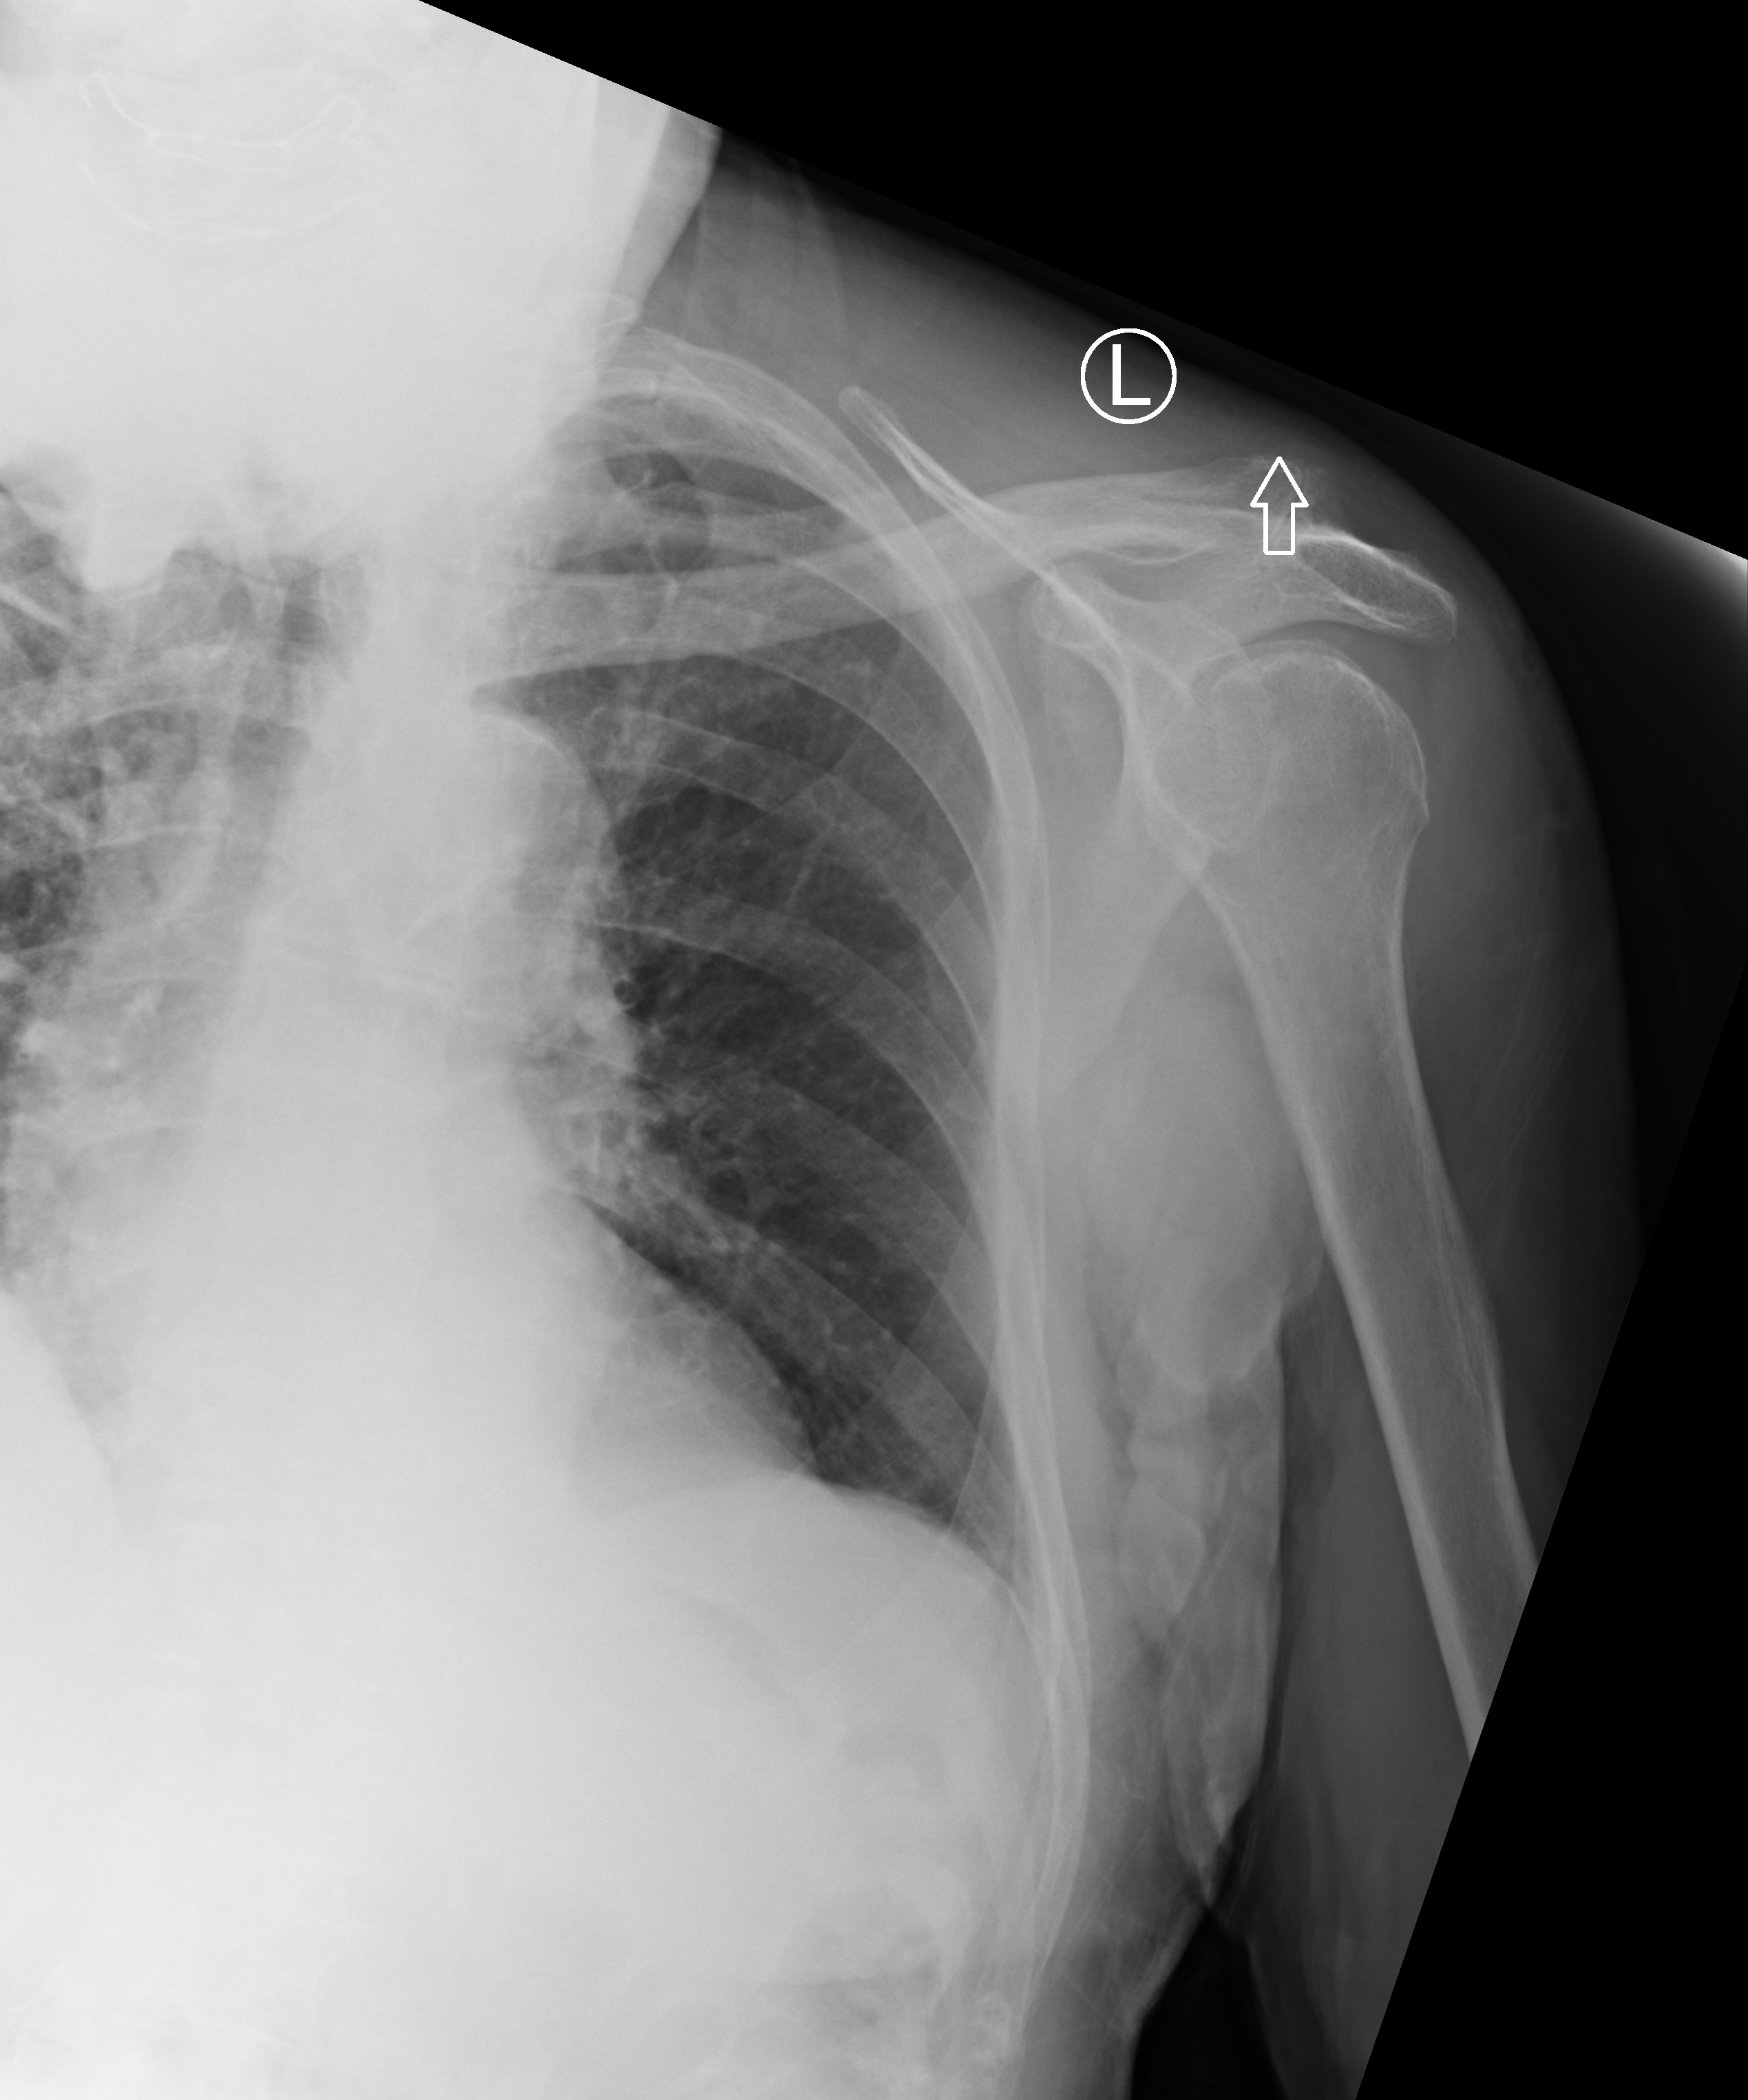
Chest X-ray (portable), anteroposterior (AP) projection. Male patient hospitalised with COVID-19, age 75–90 years.
Hospital-stay facts (about this admission, not read from this image; timing relative to this image not recorded):
- length of hospital stay: 28 days
- admitted to intensive care during this hospital stay: yes
- mechanically ventilated during this hospital stay: yes